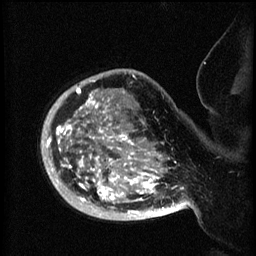
Breast MRI (dynamic contrast-enhanced), one sagittal slice; slice 51 of 60 in the series (ordered by position); 3 images stored at this slice position (order not interpretable as contrast timing); 1.5 T; TE 4.2 ms, TR 8.2 ms; 2 mm slice thickness; 256 × 256 image matrix, field of view 200 × 200 mm. Patient: female, 50 years.
Annotated regions visible in this slice (semi-automatically segmented with operator editing):
- analysis volume of interest (the breast-tissue region the enhancement analysis was run in; not a lesion): bounding box <44,72,173,219> (left, top, right, bottom; pixels)
- tumour enhancement mask (voxels above the 70 % enhancement threshold inside the analysis volume of interest): <45,80,173,215>